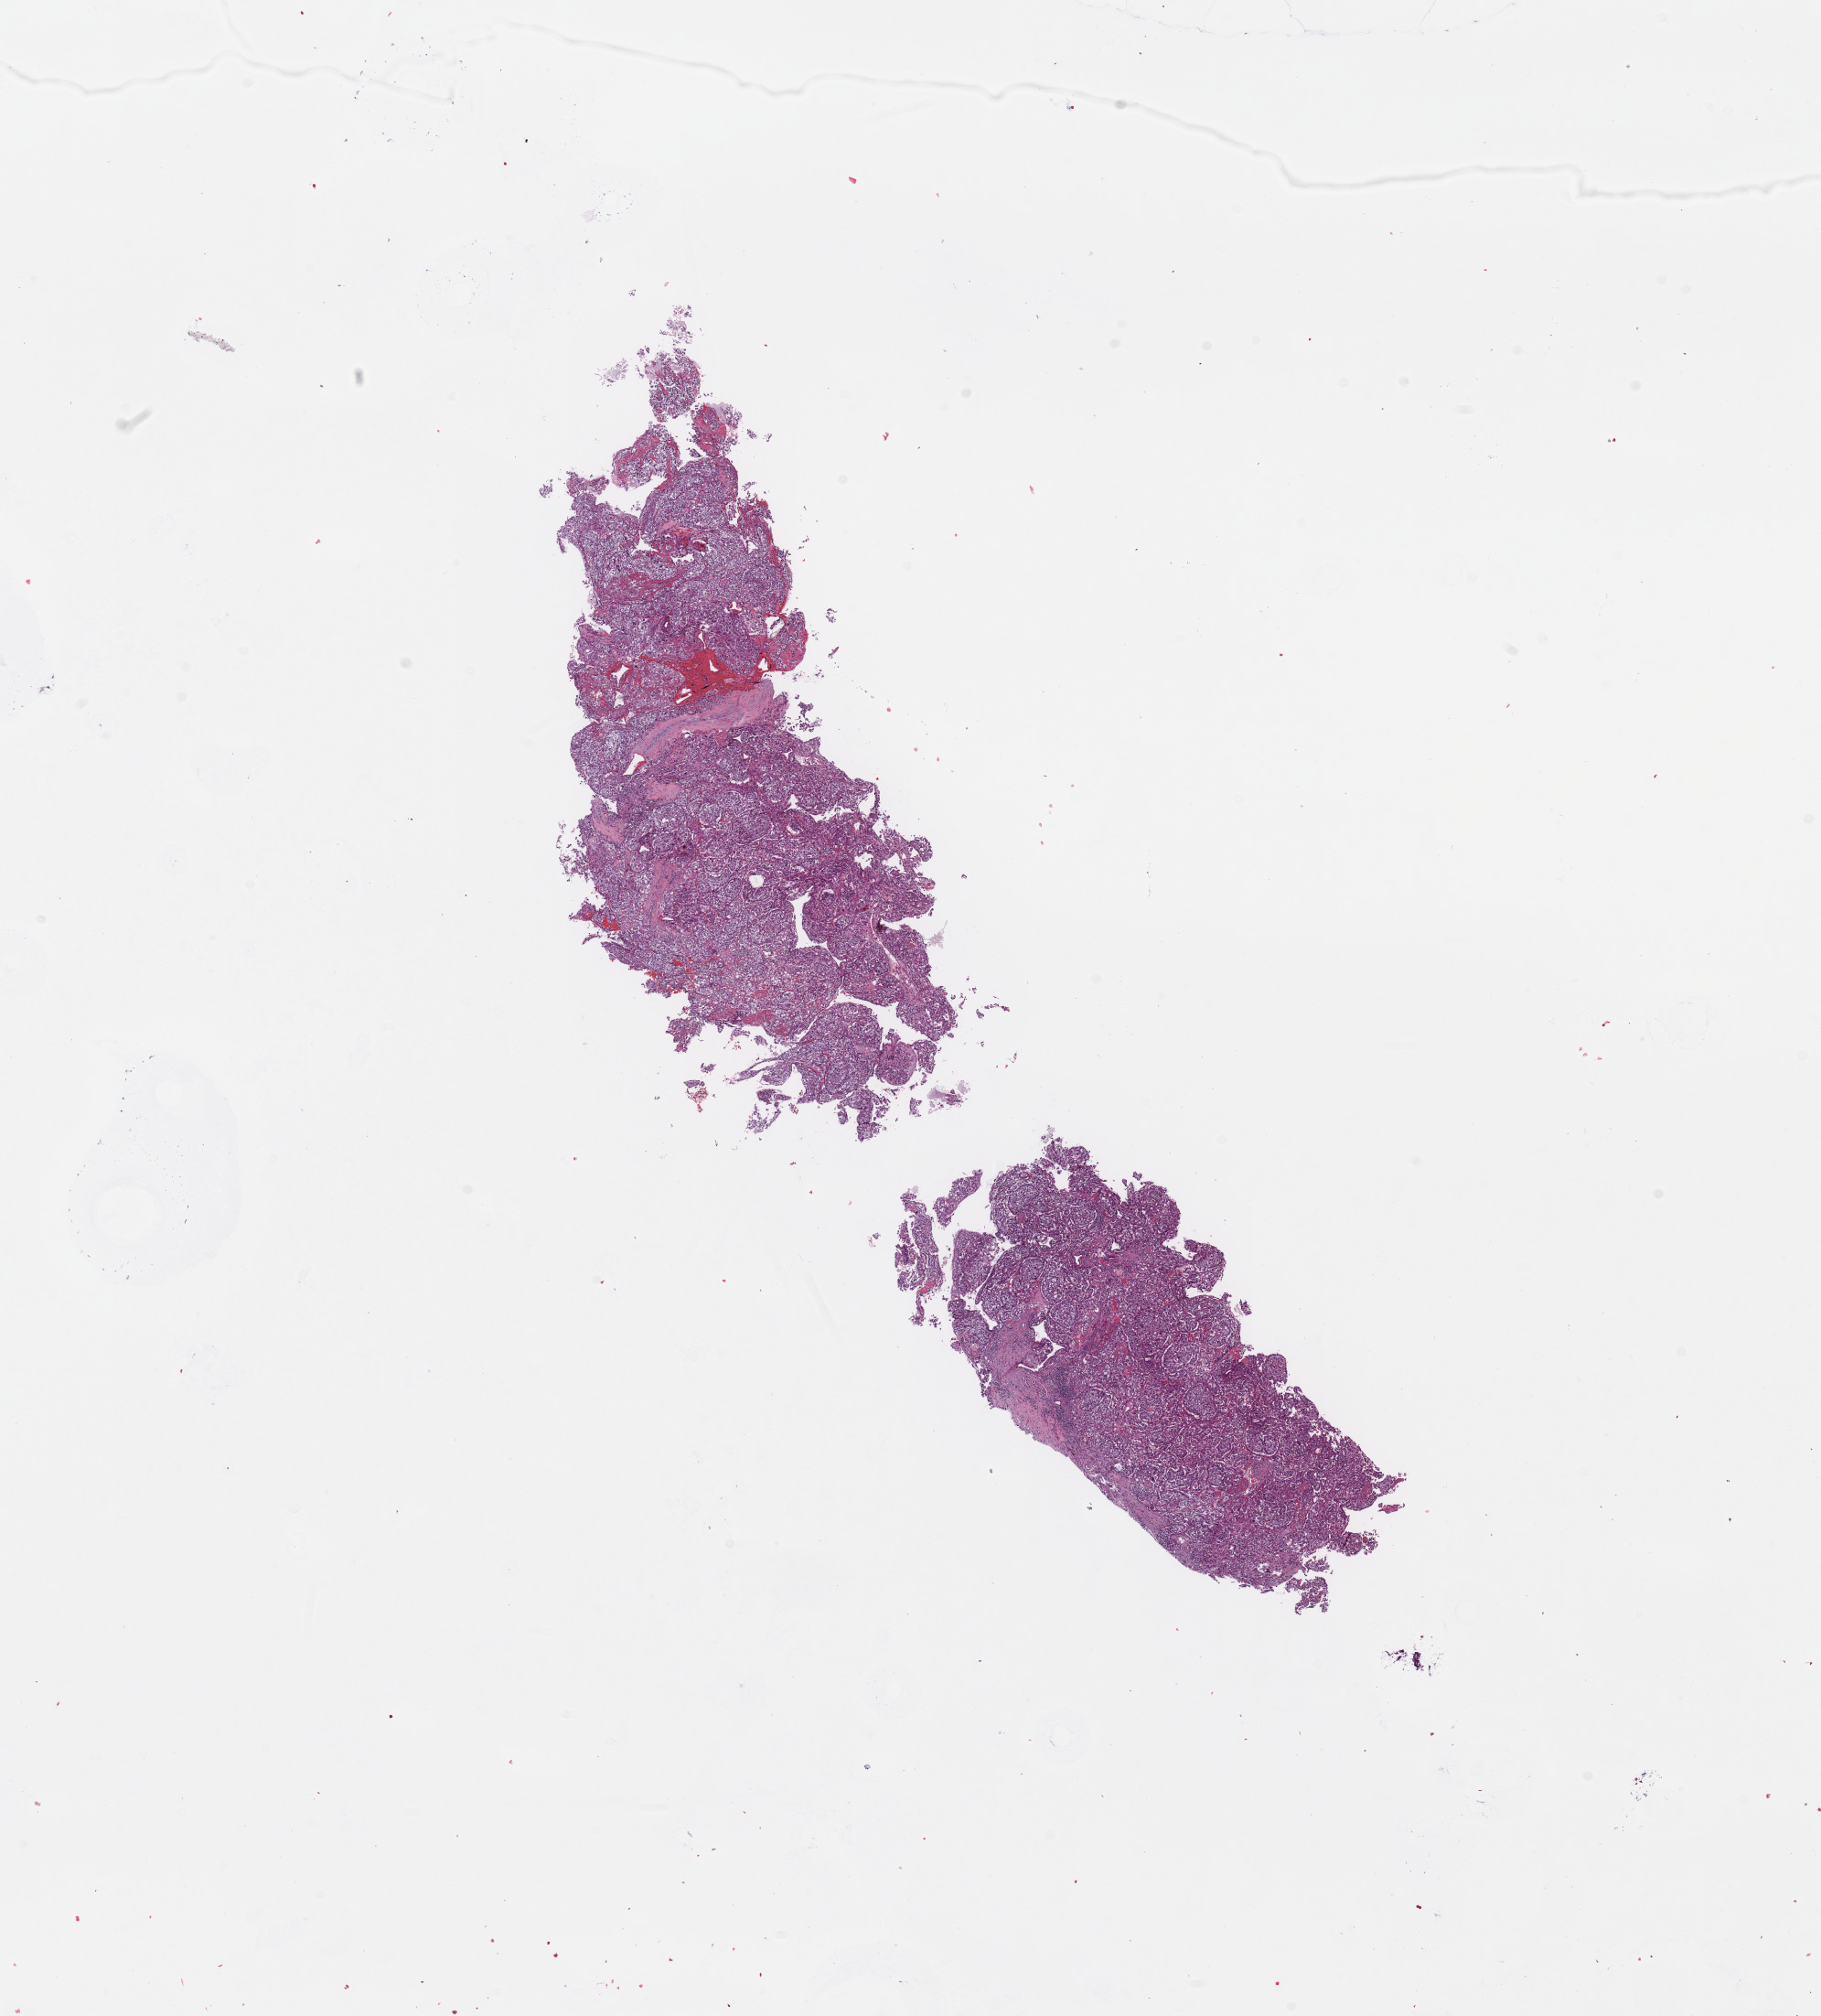
Digitized H&E-stained tissue section (whole slide), a low-resolution overview of the entire scanned area, about 15.8 x 17.4 mm (slide scanned at 20x); kidney, tumour tissue. Male, 47 y/o. Histologic grade: G4 (undifferentiated).
• primary tumour site (as recorded): lower pole
• AJCC pathologic stage: III
• histologic diagnosis: Renal cell carcinoma, NOS